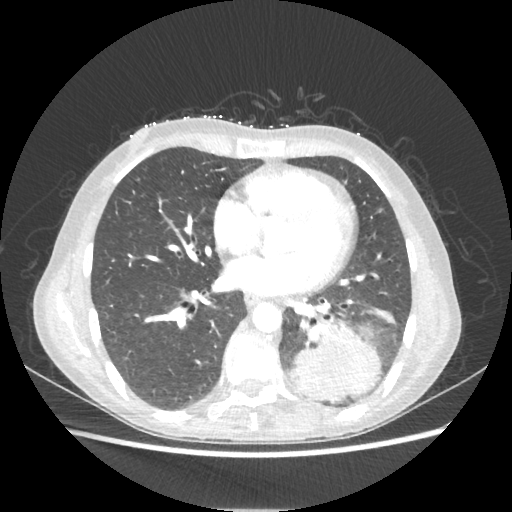
Chest CT, one axial slice. Position 95 of 221 along the scan axis. Reconstruction kernel STANDARD. Lung window (W 1500 / L -600 HU). 512 × 512 image matrix. Female patient, age 53 years. Case-level facts recorded for this patient, not image findings: clinical TNM (as recorded): T3 N0 M0.
Outlined on this slice (rectangle marked by the reading radiologist):
- lung tumour (recorded histology: adenocarcinoma): bounding box <287,321,379,403> (left, top, right, bottom; pixels)